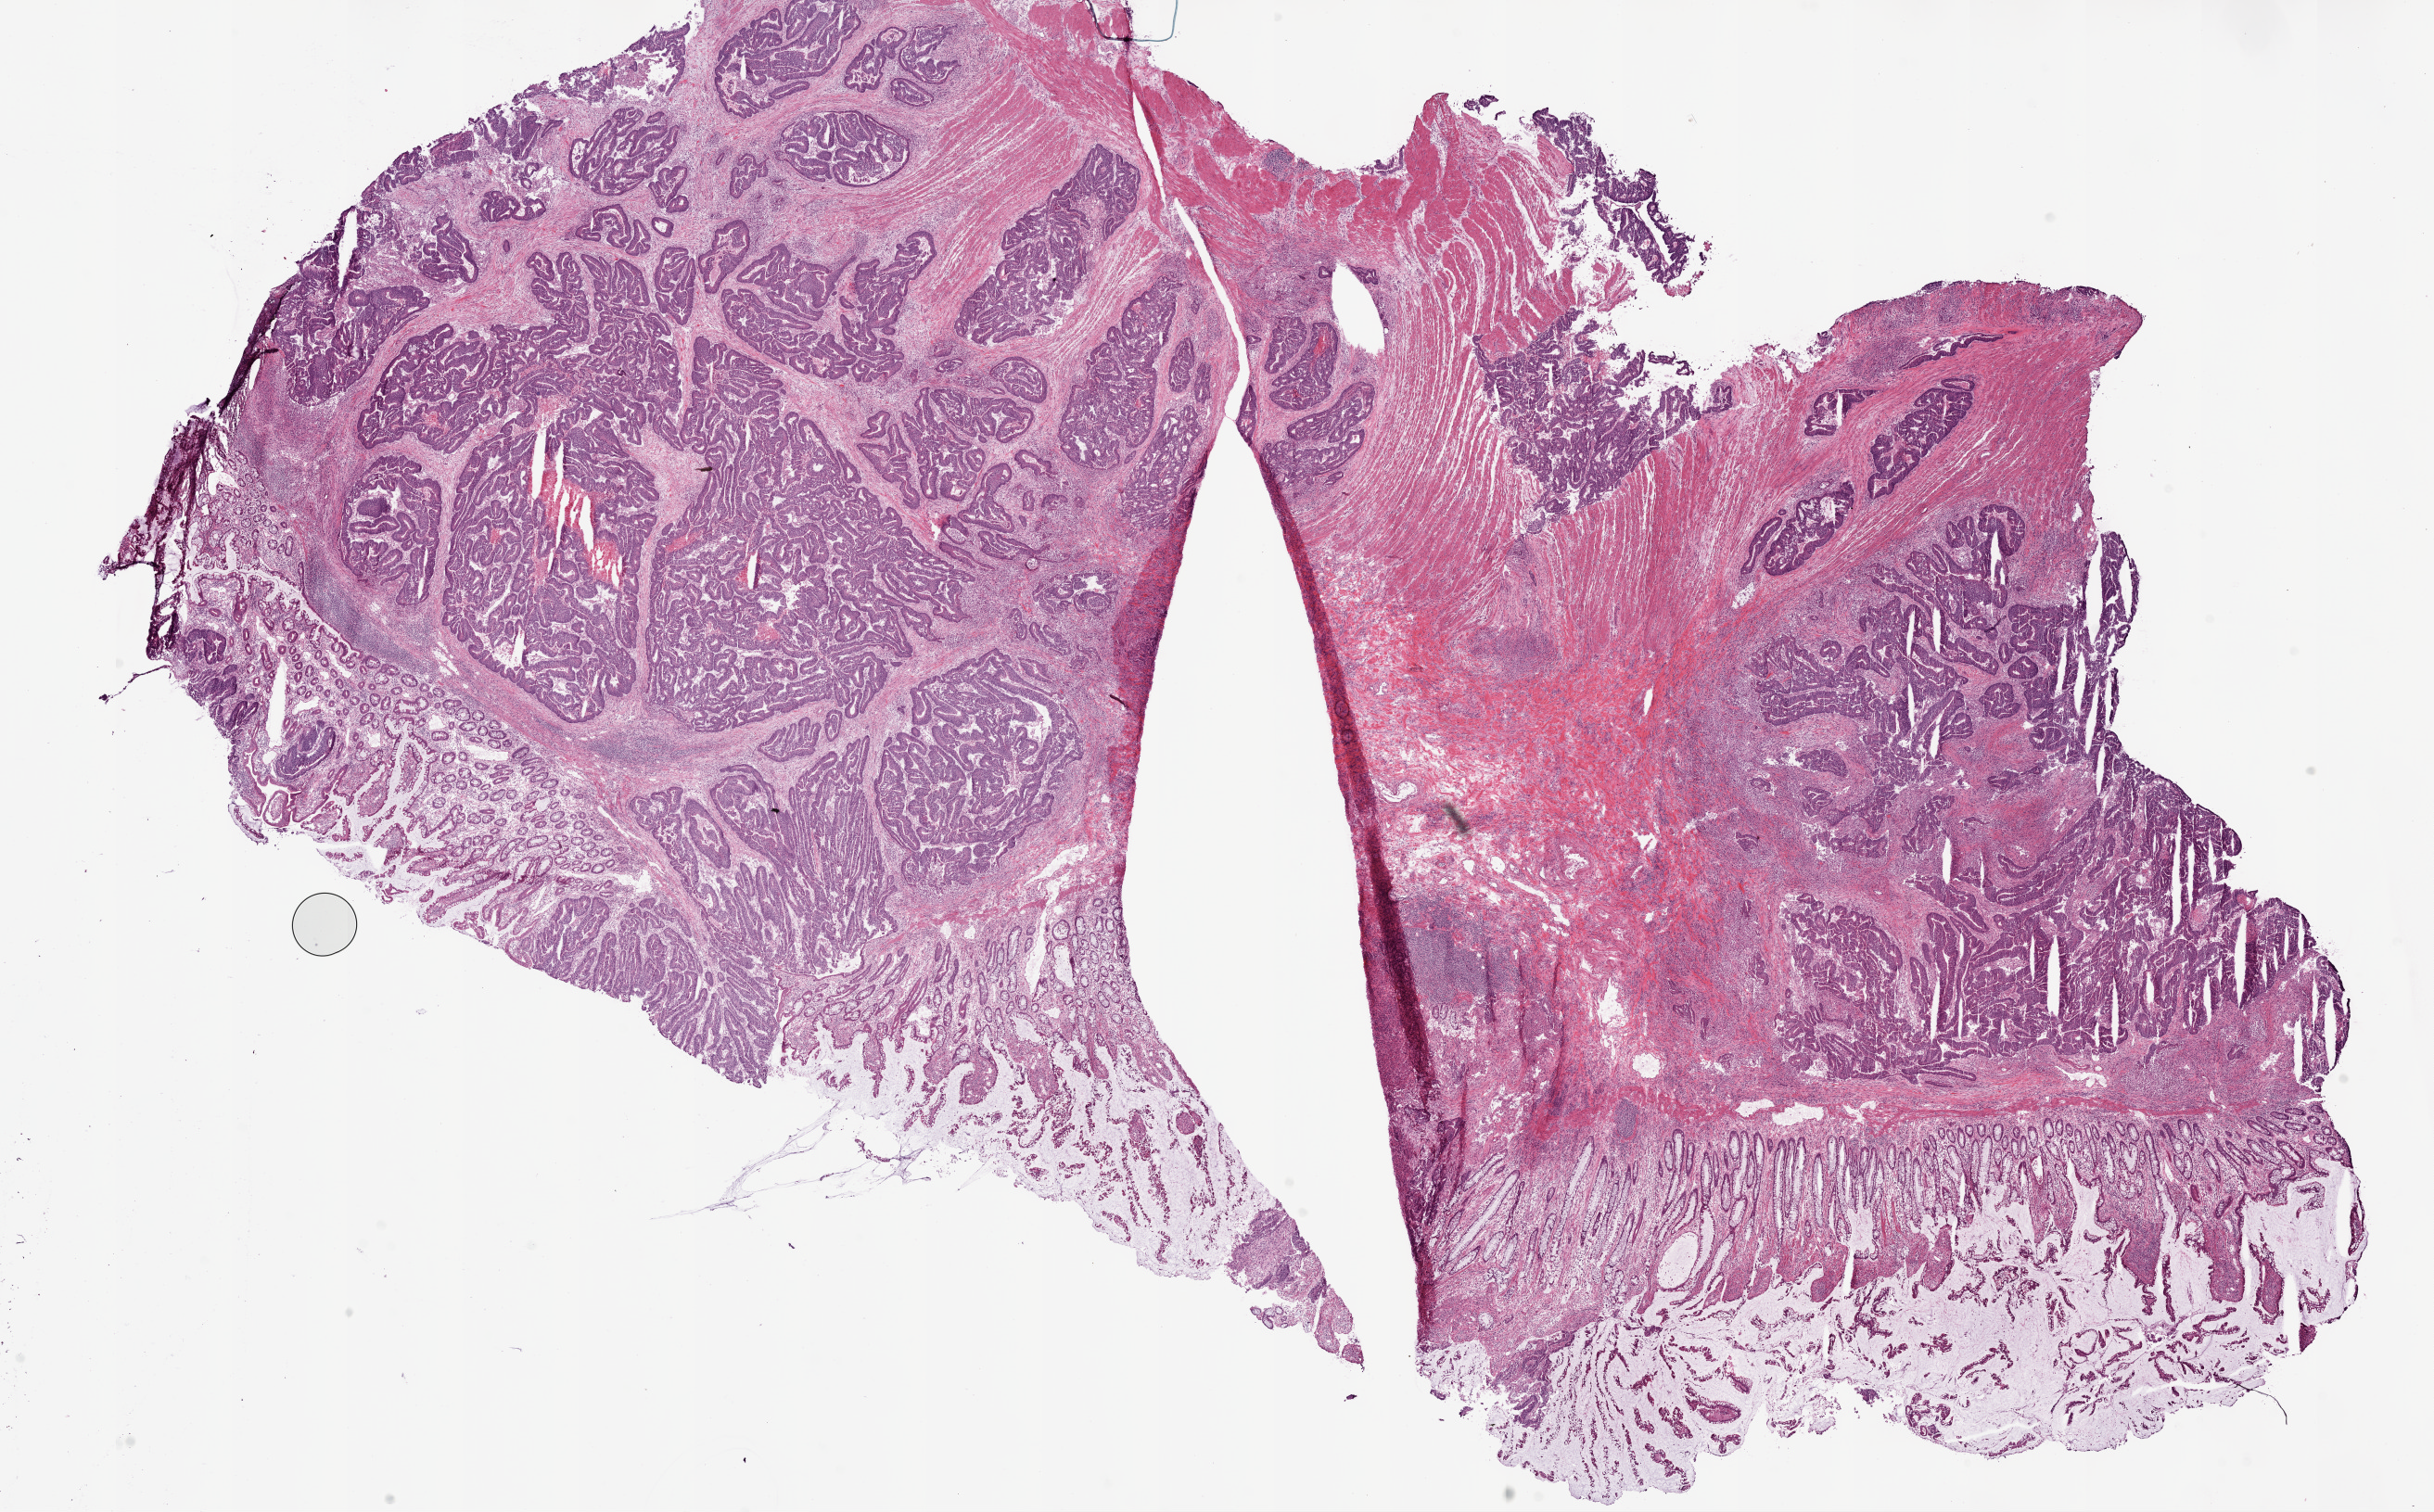
H&E whole-slide image, low-resolution overview of the scanned area, about 21.1 x 13.1 mm (from a 20x scan), frozen section, sample: primary tumour, colon. Female patient; age at initial diagnosis 68 years. Slide review estimates, as recorded: tumour cells 66%, tumour nuclei 60%, normal cells 25%, stromal cells 8%, necrosis 1%. Infiltration values recorded for this section: lymphocyte infiltration 10%, monocyte infiltration 1%, neutrophil infiltration 2%.
Pathologic diagnosis: Adenocarcinoma, NOS. AJCC pathologic stage: IIA.